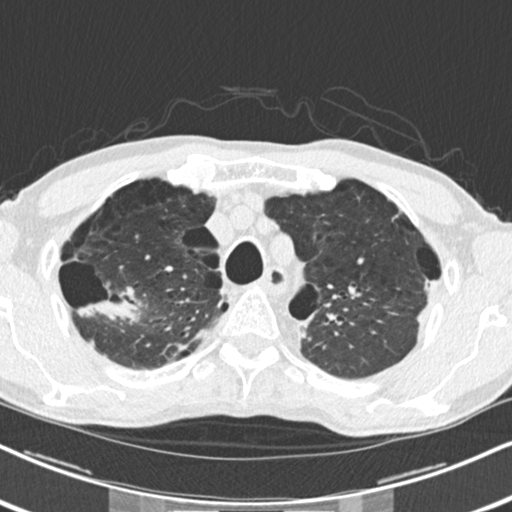
Chest CT (low-dose screening protocol), one axial image; baseline screening round; lung window (W 1500 / L -600 HU); 120 kVp; slice 49 of 250 in the series; 512 × 512 image matrix, field of view 325 × 325 mm. Male participant, aged 71 years at enrolment. Current smoker at enrolment.
Expert-annotated lung lesion, bounding box <92,264,152,318> (left, top, right, bottom; pixels). The screening reader recorded 2 non-calcified nodules or masses ≥4 mm on this exam; which of them this box marks is not recorded. Later outcome: lung cancer diagnosed 454 days after this screen — adenocarcinoma, NOS, right upper lobe, well differentiated (G1), stage IA (AJCC 6th edition), 30 mm at pathology.